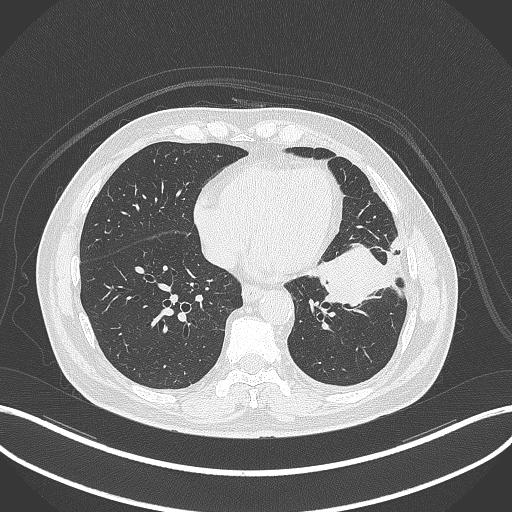
Chest CT, one axial slice; position 127 of 230 along the scan axis; reconstruction kernel B70f; lung window (W 1500 / L -600 HU); 1 mm slice thickness; 512 × 512 image matrix, field of view 400 × 400 mm. Patient: male, 68 years. From the clinical record (not read from this slice): clinical TNM (as recorded): T2b N0 M0.
Outlined on this slice (bounding box drawn by a radiologist):
- lung tumour (recorded histology: squamous cell carcinoma): bounding box [x1, y1, x2, y2] px = [307, 246, 408, 311]